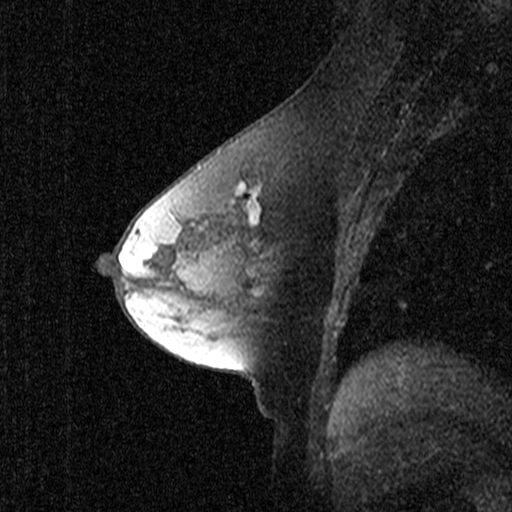
Breast MRI (dynamic contrast-enhanced), one sagittal slice. Position 25 of 44 along the scan axis. Dynamic contrast-enhanced study with each time point stored as its own series, time point 2 of 3 at this slice position (early post-contrast, ordered by acquisition time). 1.5 T. TE 4.5 ms, TR 11 ms. 2.27 mm slice thickness. 512 × 512 image matrix, field of view 200 × 200 mm. Female patient, age 53 years. Case-level facts recorded for this patient, not image findings: setting: breast cancer imaged before/during neoadjuvant chemotherapy; receptor status: HR-positive, HER2-negative.
Annotated regions visible in this slice (semi-automatically segmented with operator editing):
- analysis volume of interest (the breast-tissue region the enhancement analysis was run in; not a lesion): bounding box <192,146,303,281> (left, top, right, bottom; pixels)
- tumour enhancement mask (voxels above the 90 % enhancement threshold inside the analysis volume of interest): <239,183,261,244>